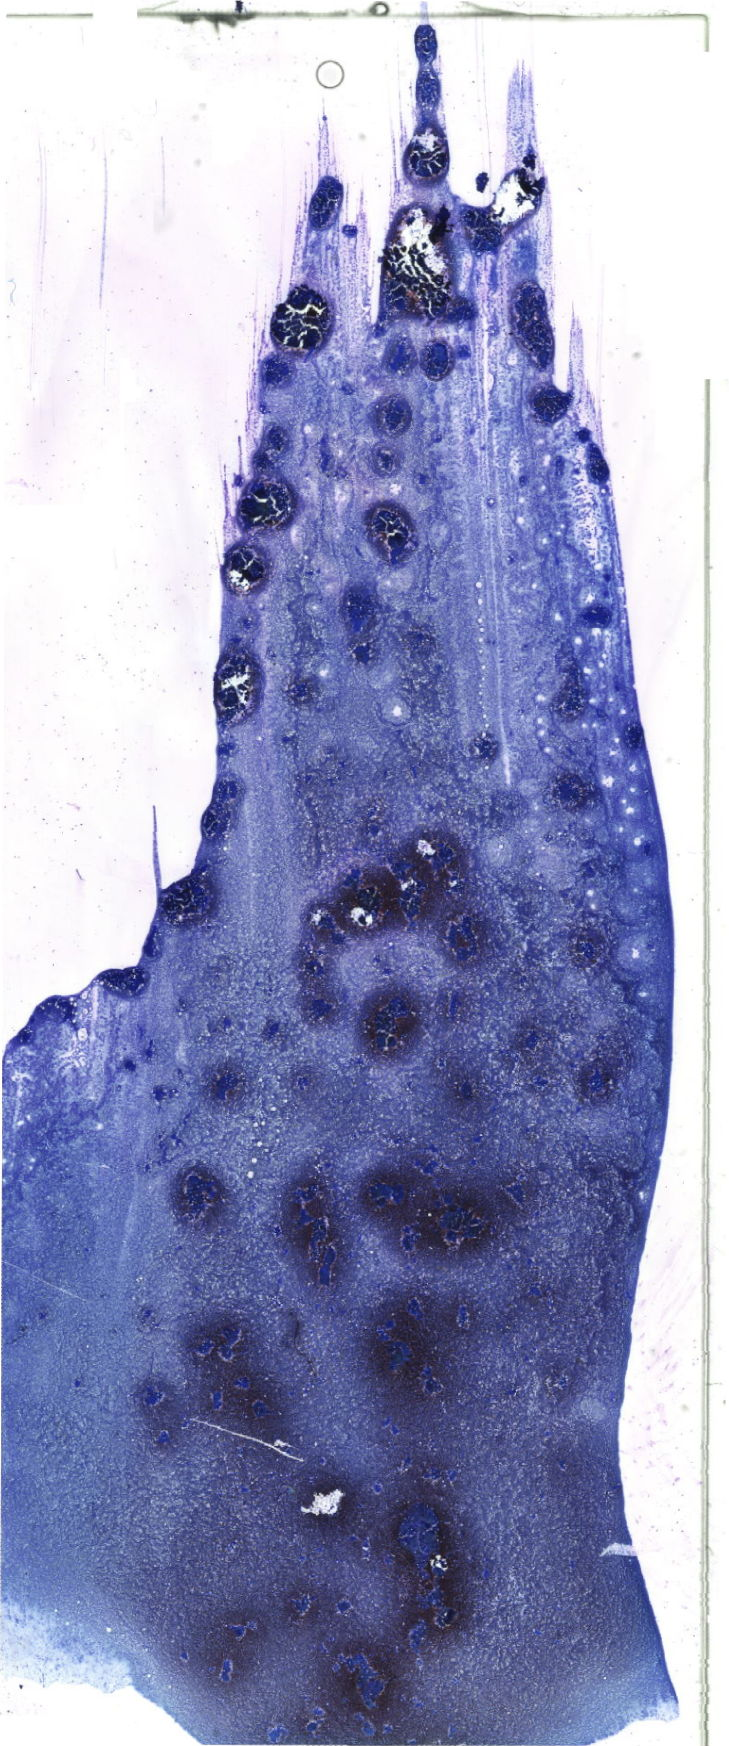
May-Grünwald-Giemsa (MGG)-stained marrow aspirate smear (whole slide), a low-resolution overview of the entire scanned area, about 20.7 x 49.5 mm. Male patient.
Diagnosis: Acute Myeloid Leukemia with Maturation.